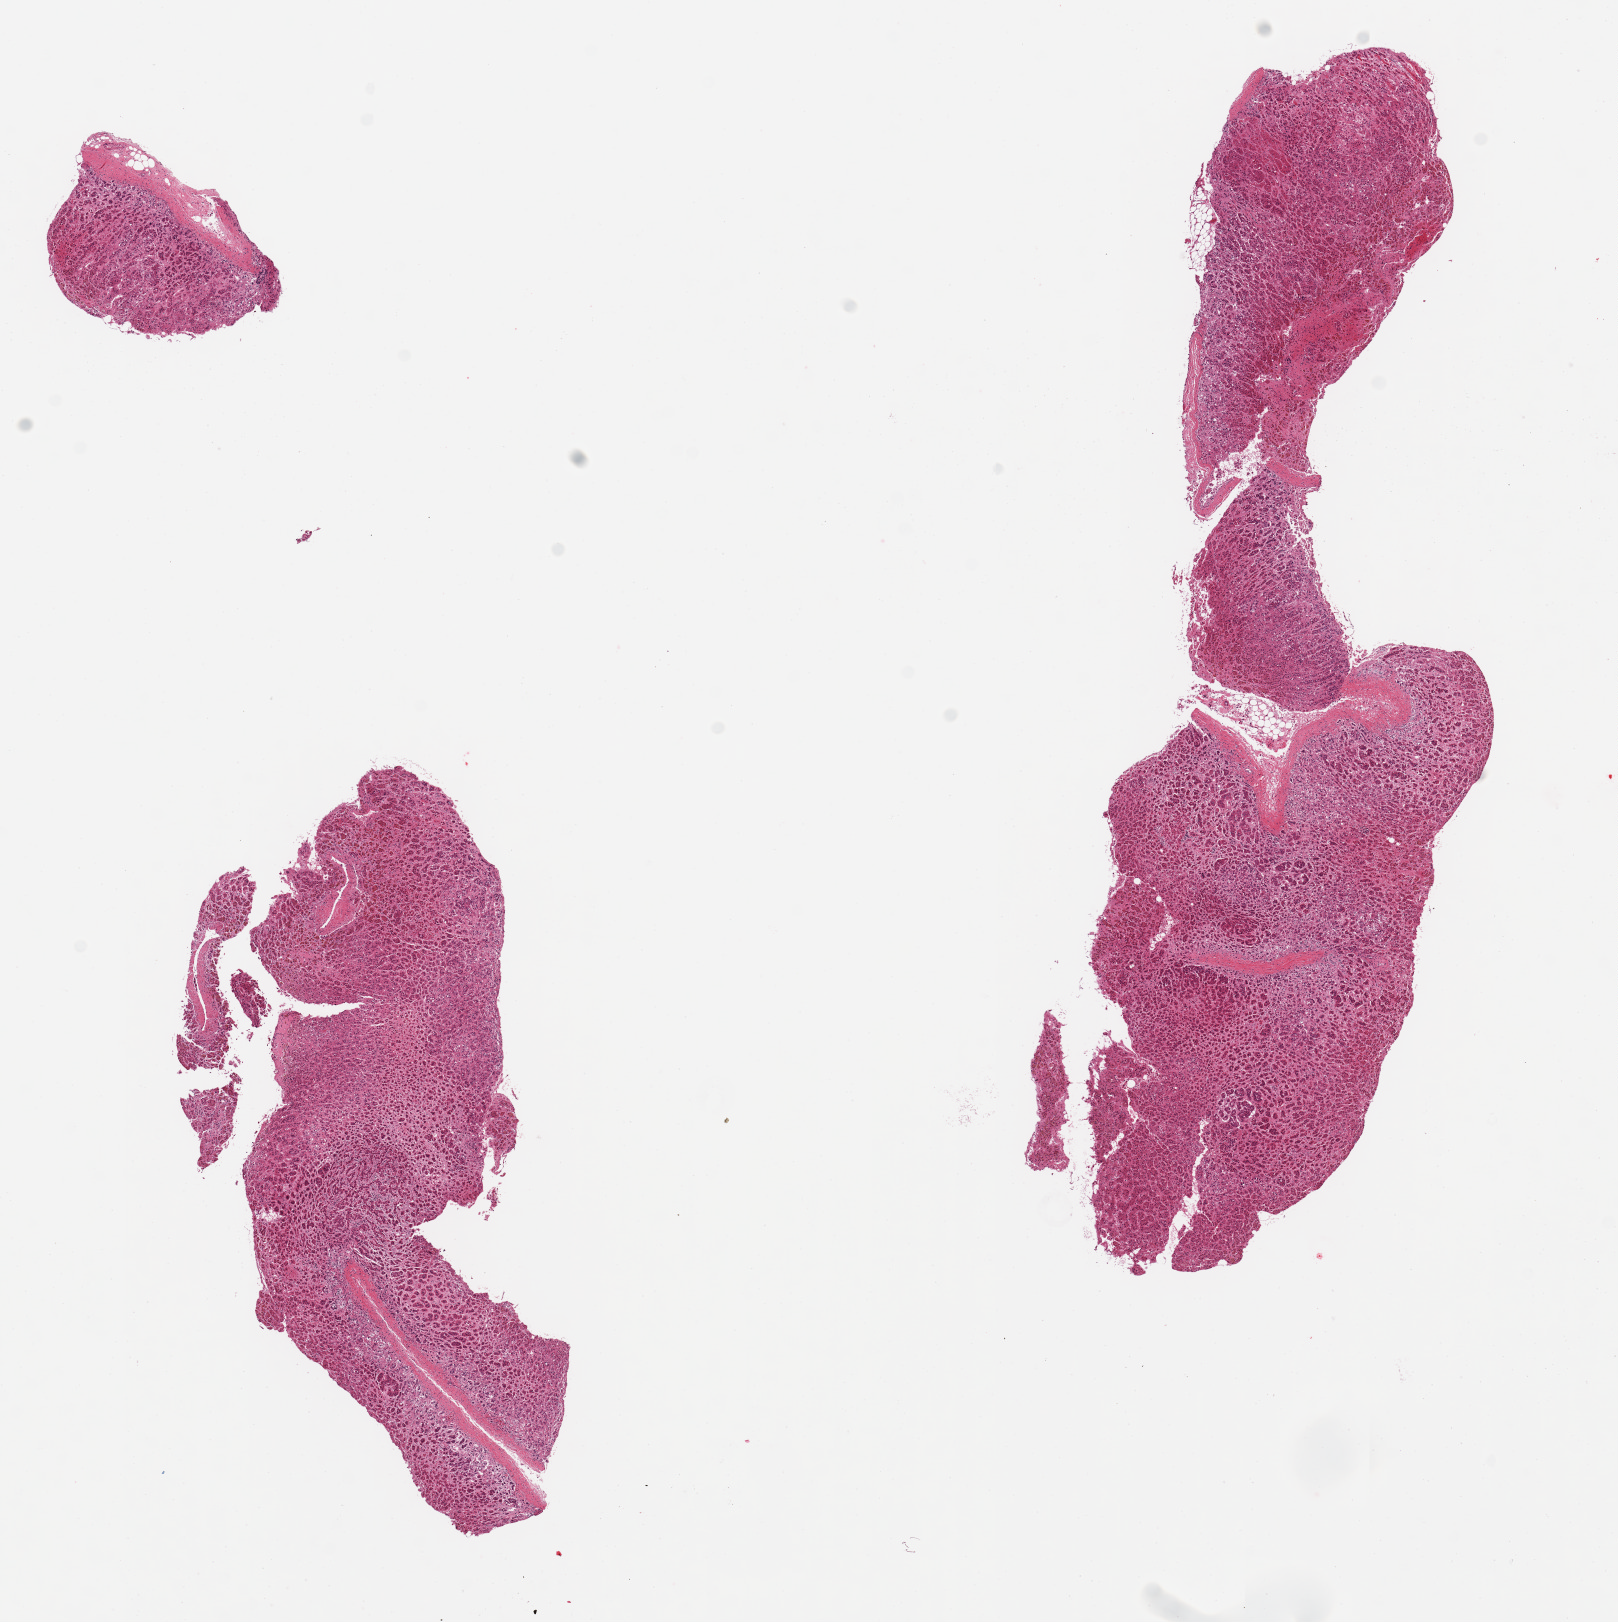
Digitized haematoxylin and eosin-stained section, brightfield — a low-resolution overview of the entire scanned area, about 12.8 x 12.8 mm, PAXgene-fixed, paraffin-embedded tissue, target tissue: adrenal gland, tissue donor sample.
Reviewer comment on this tissue sample: 2 pieces, all cortex, moderate-advanced autolysis.